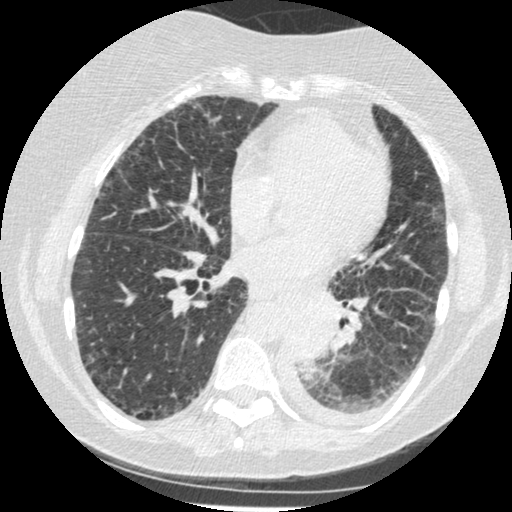
Low-dose screening chest CT, one axial slice; lung window (W 1500 / L -600 HU); 1.25 mm slice thickness; 512 × 512 image matrix.
Annotated regions visible in this slice (expert manual segmentation):
- lesion 1 (tumor, lower lobe of left lung): box from (x=287, y=308) to (x=334, y=363) px